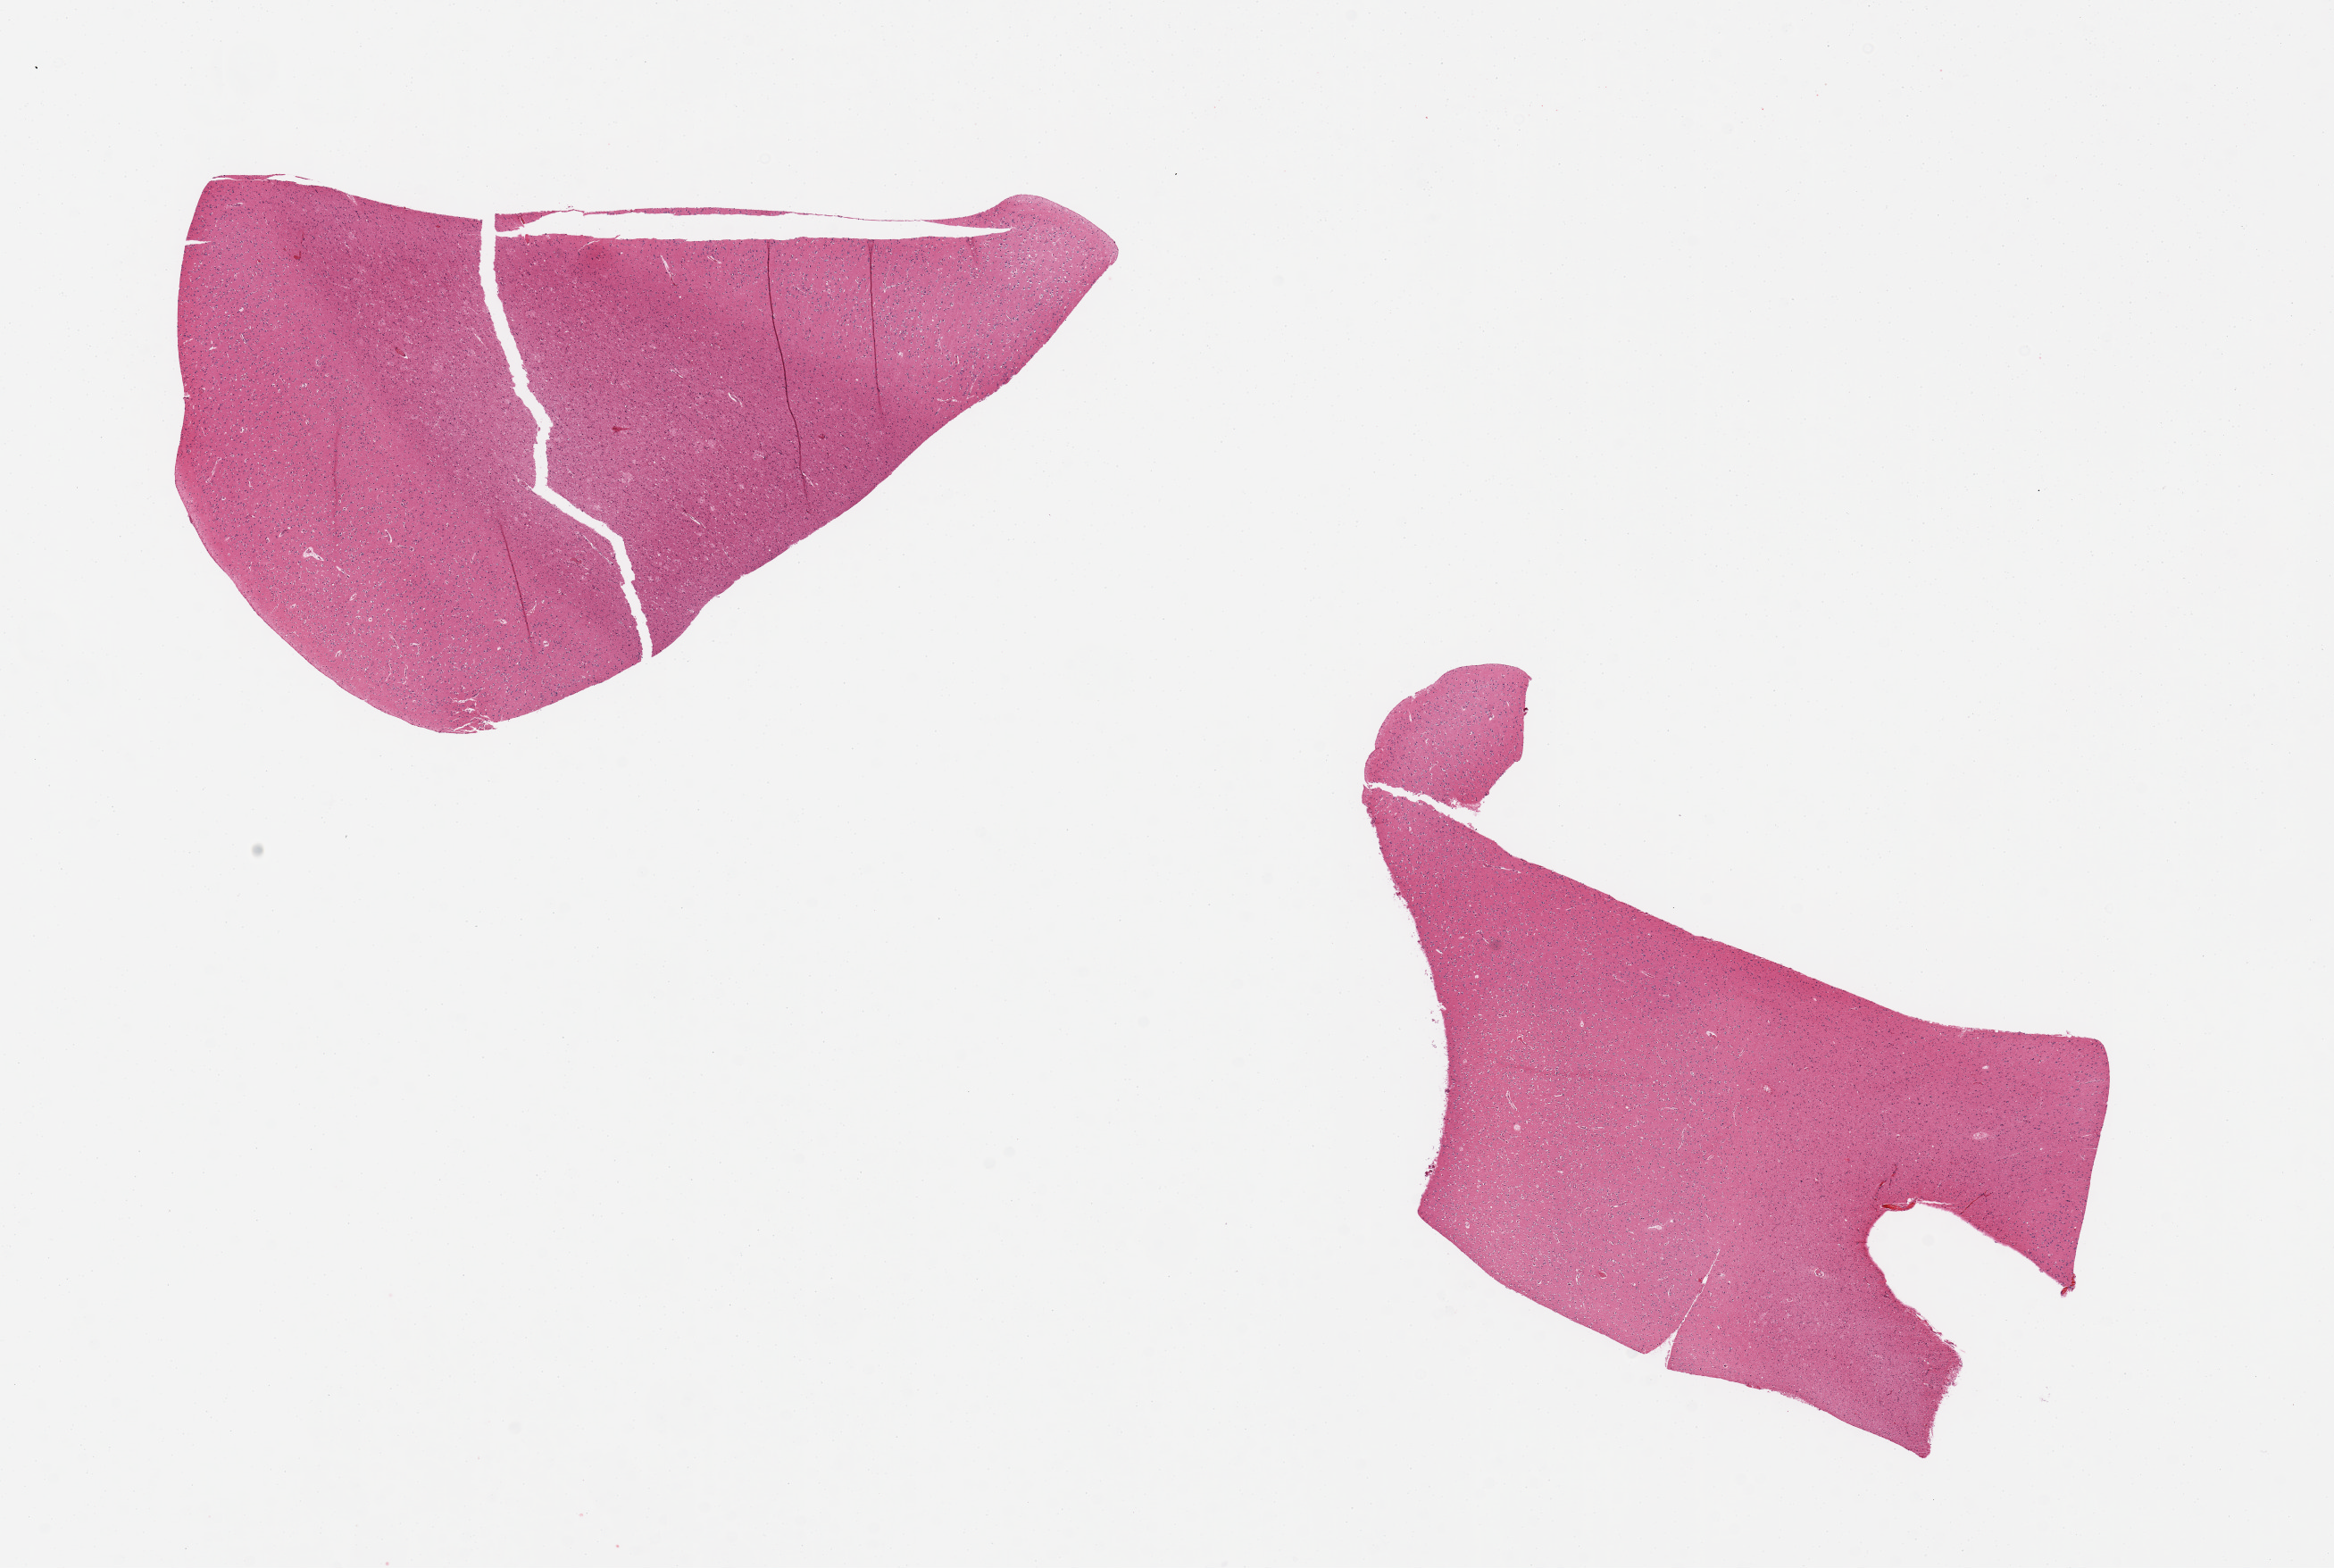
Whole-slide image, haematoxylin and eosin stain, low-resolution overview of the scanned area, about 20.7 x 13.9 mm, PAXgene-fixed paraffin-embedded (PFPE) section, target tissue: cerebral cortex, tissue donor sample.
Reviewer comment on this tissue sample: 2 pieces.